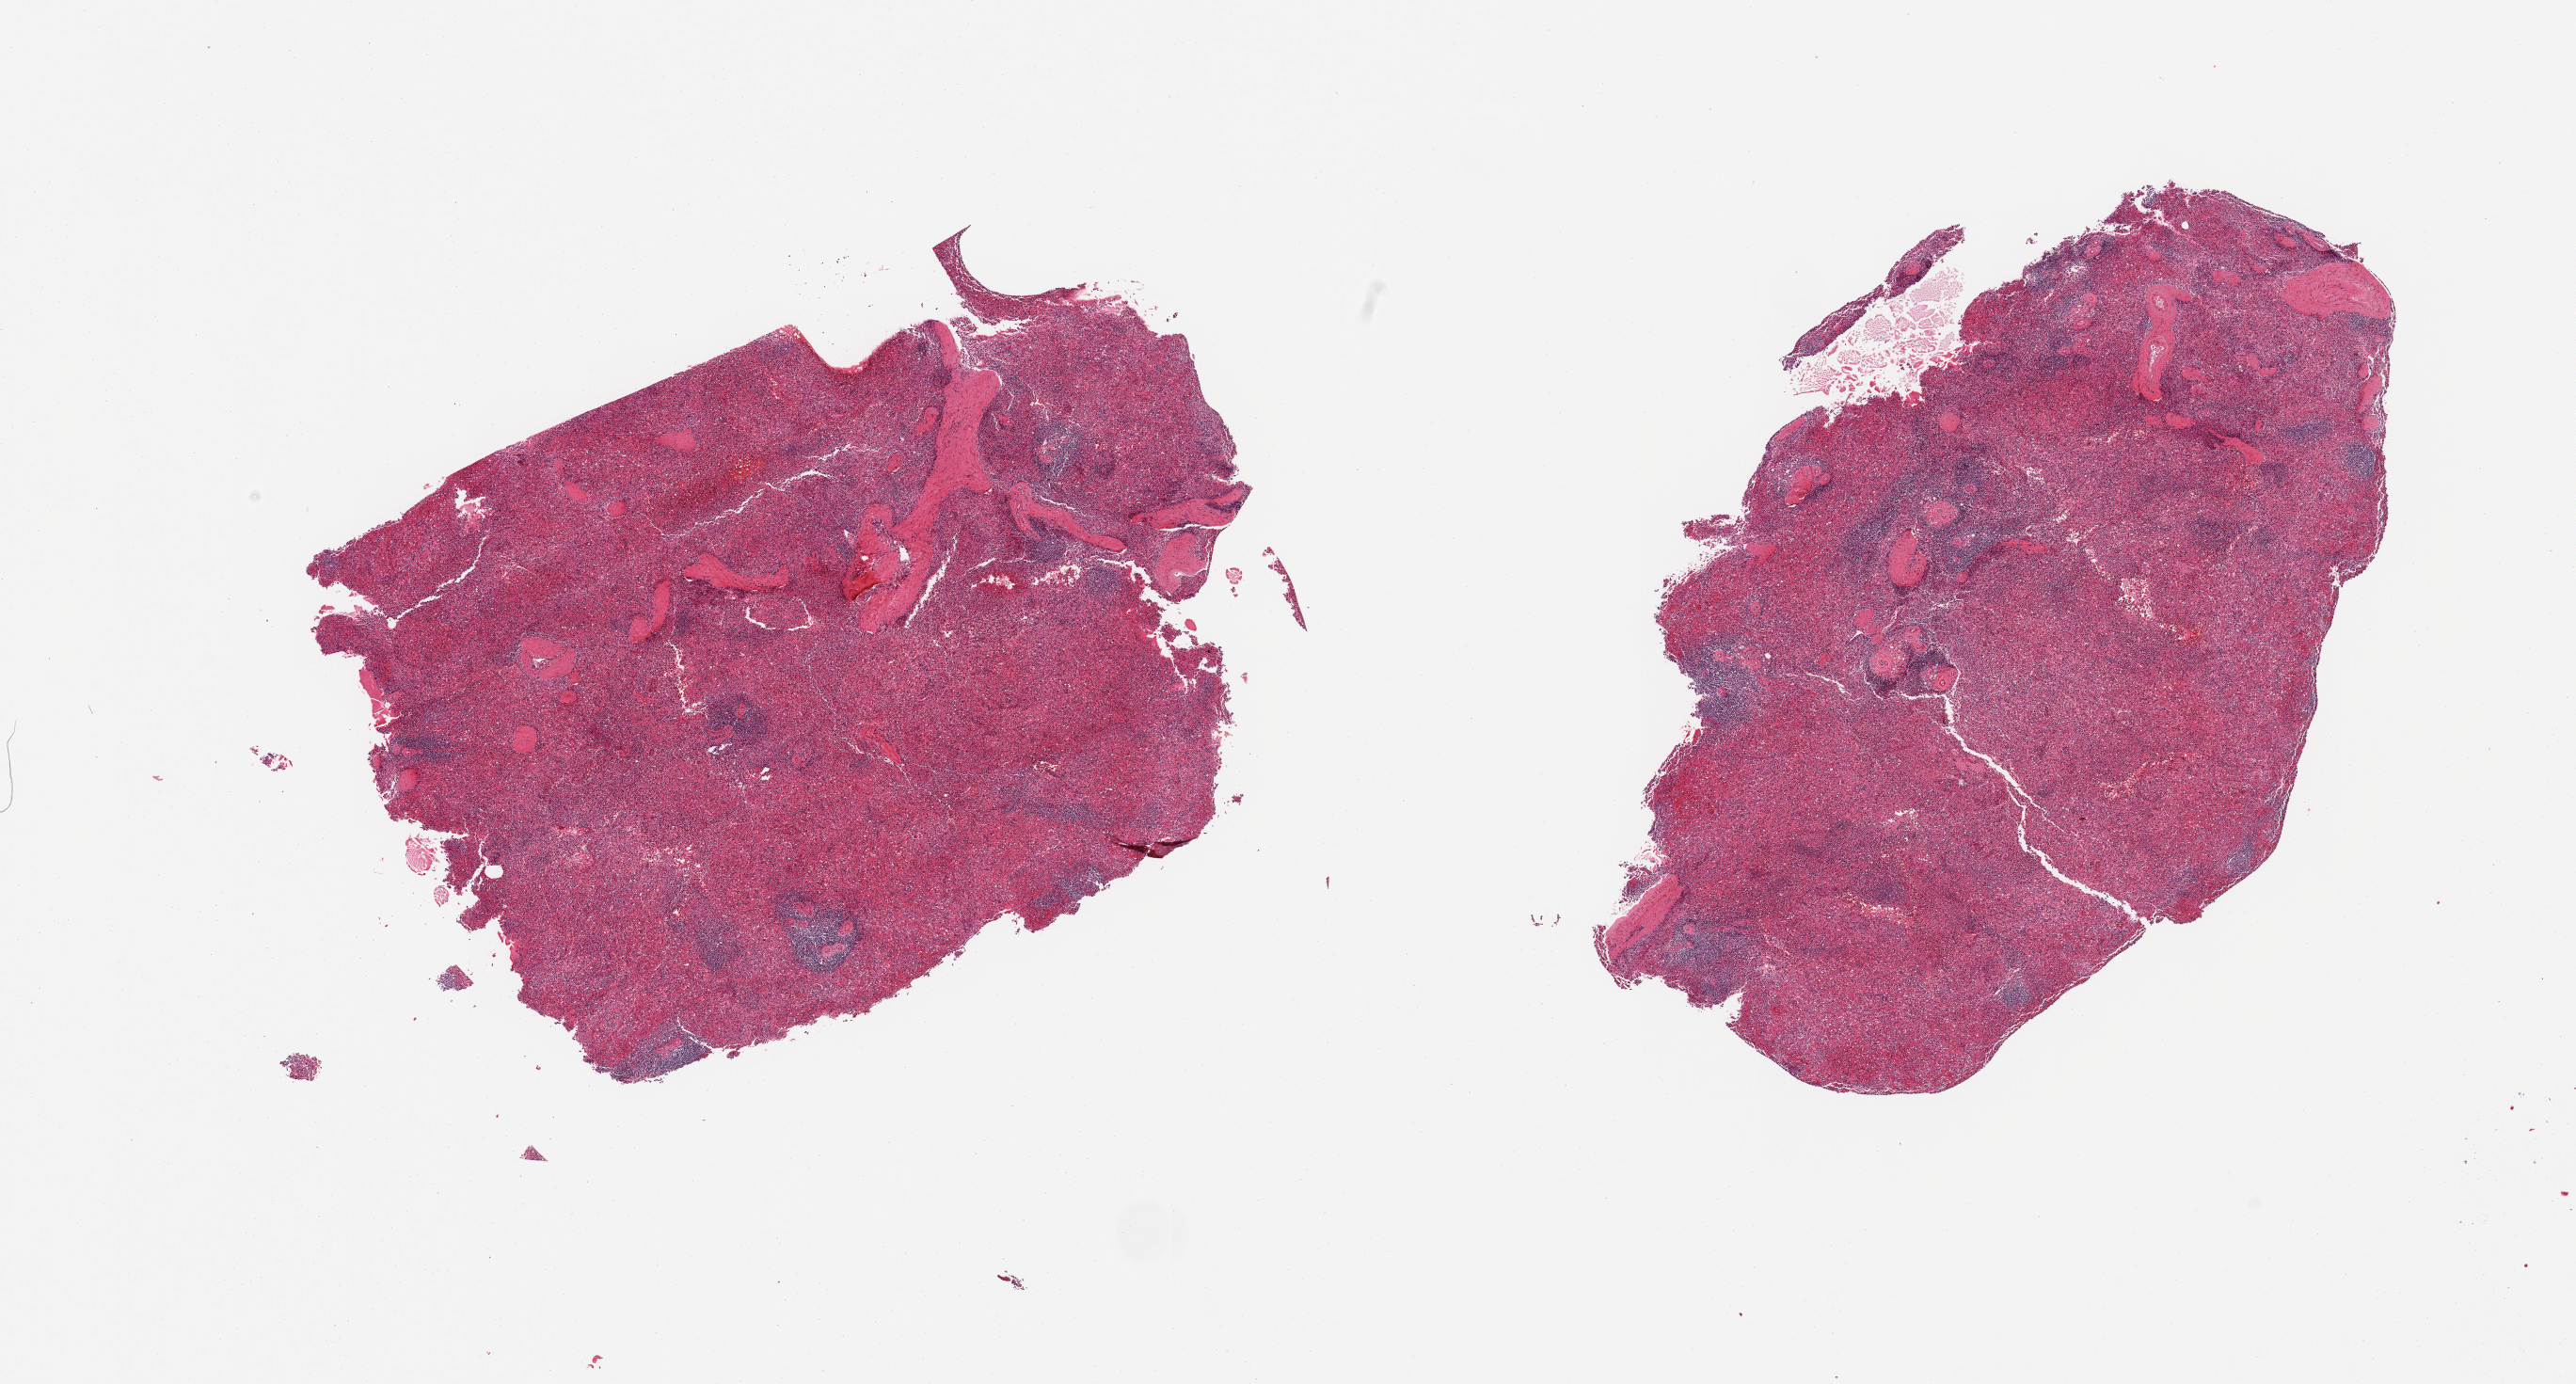
Digitized hematoxylin and eosin (H&E)-stained section — whole scanned area (about 21.7 x 11.6 mm) shown as a low-resolution overview, PAXgene-fixed, paraffin-embedded tissue, target tissue: spleen, tissue donor sample. Donor: male.
- review note (as recorded): 2 pieces; moderate congestion